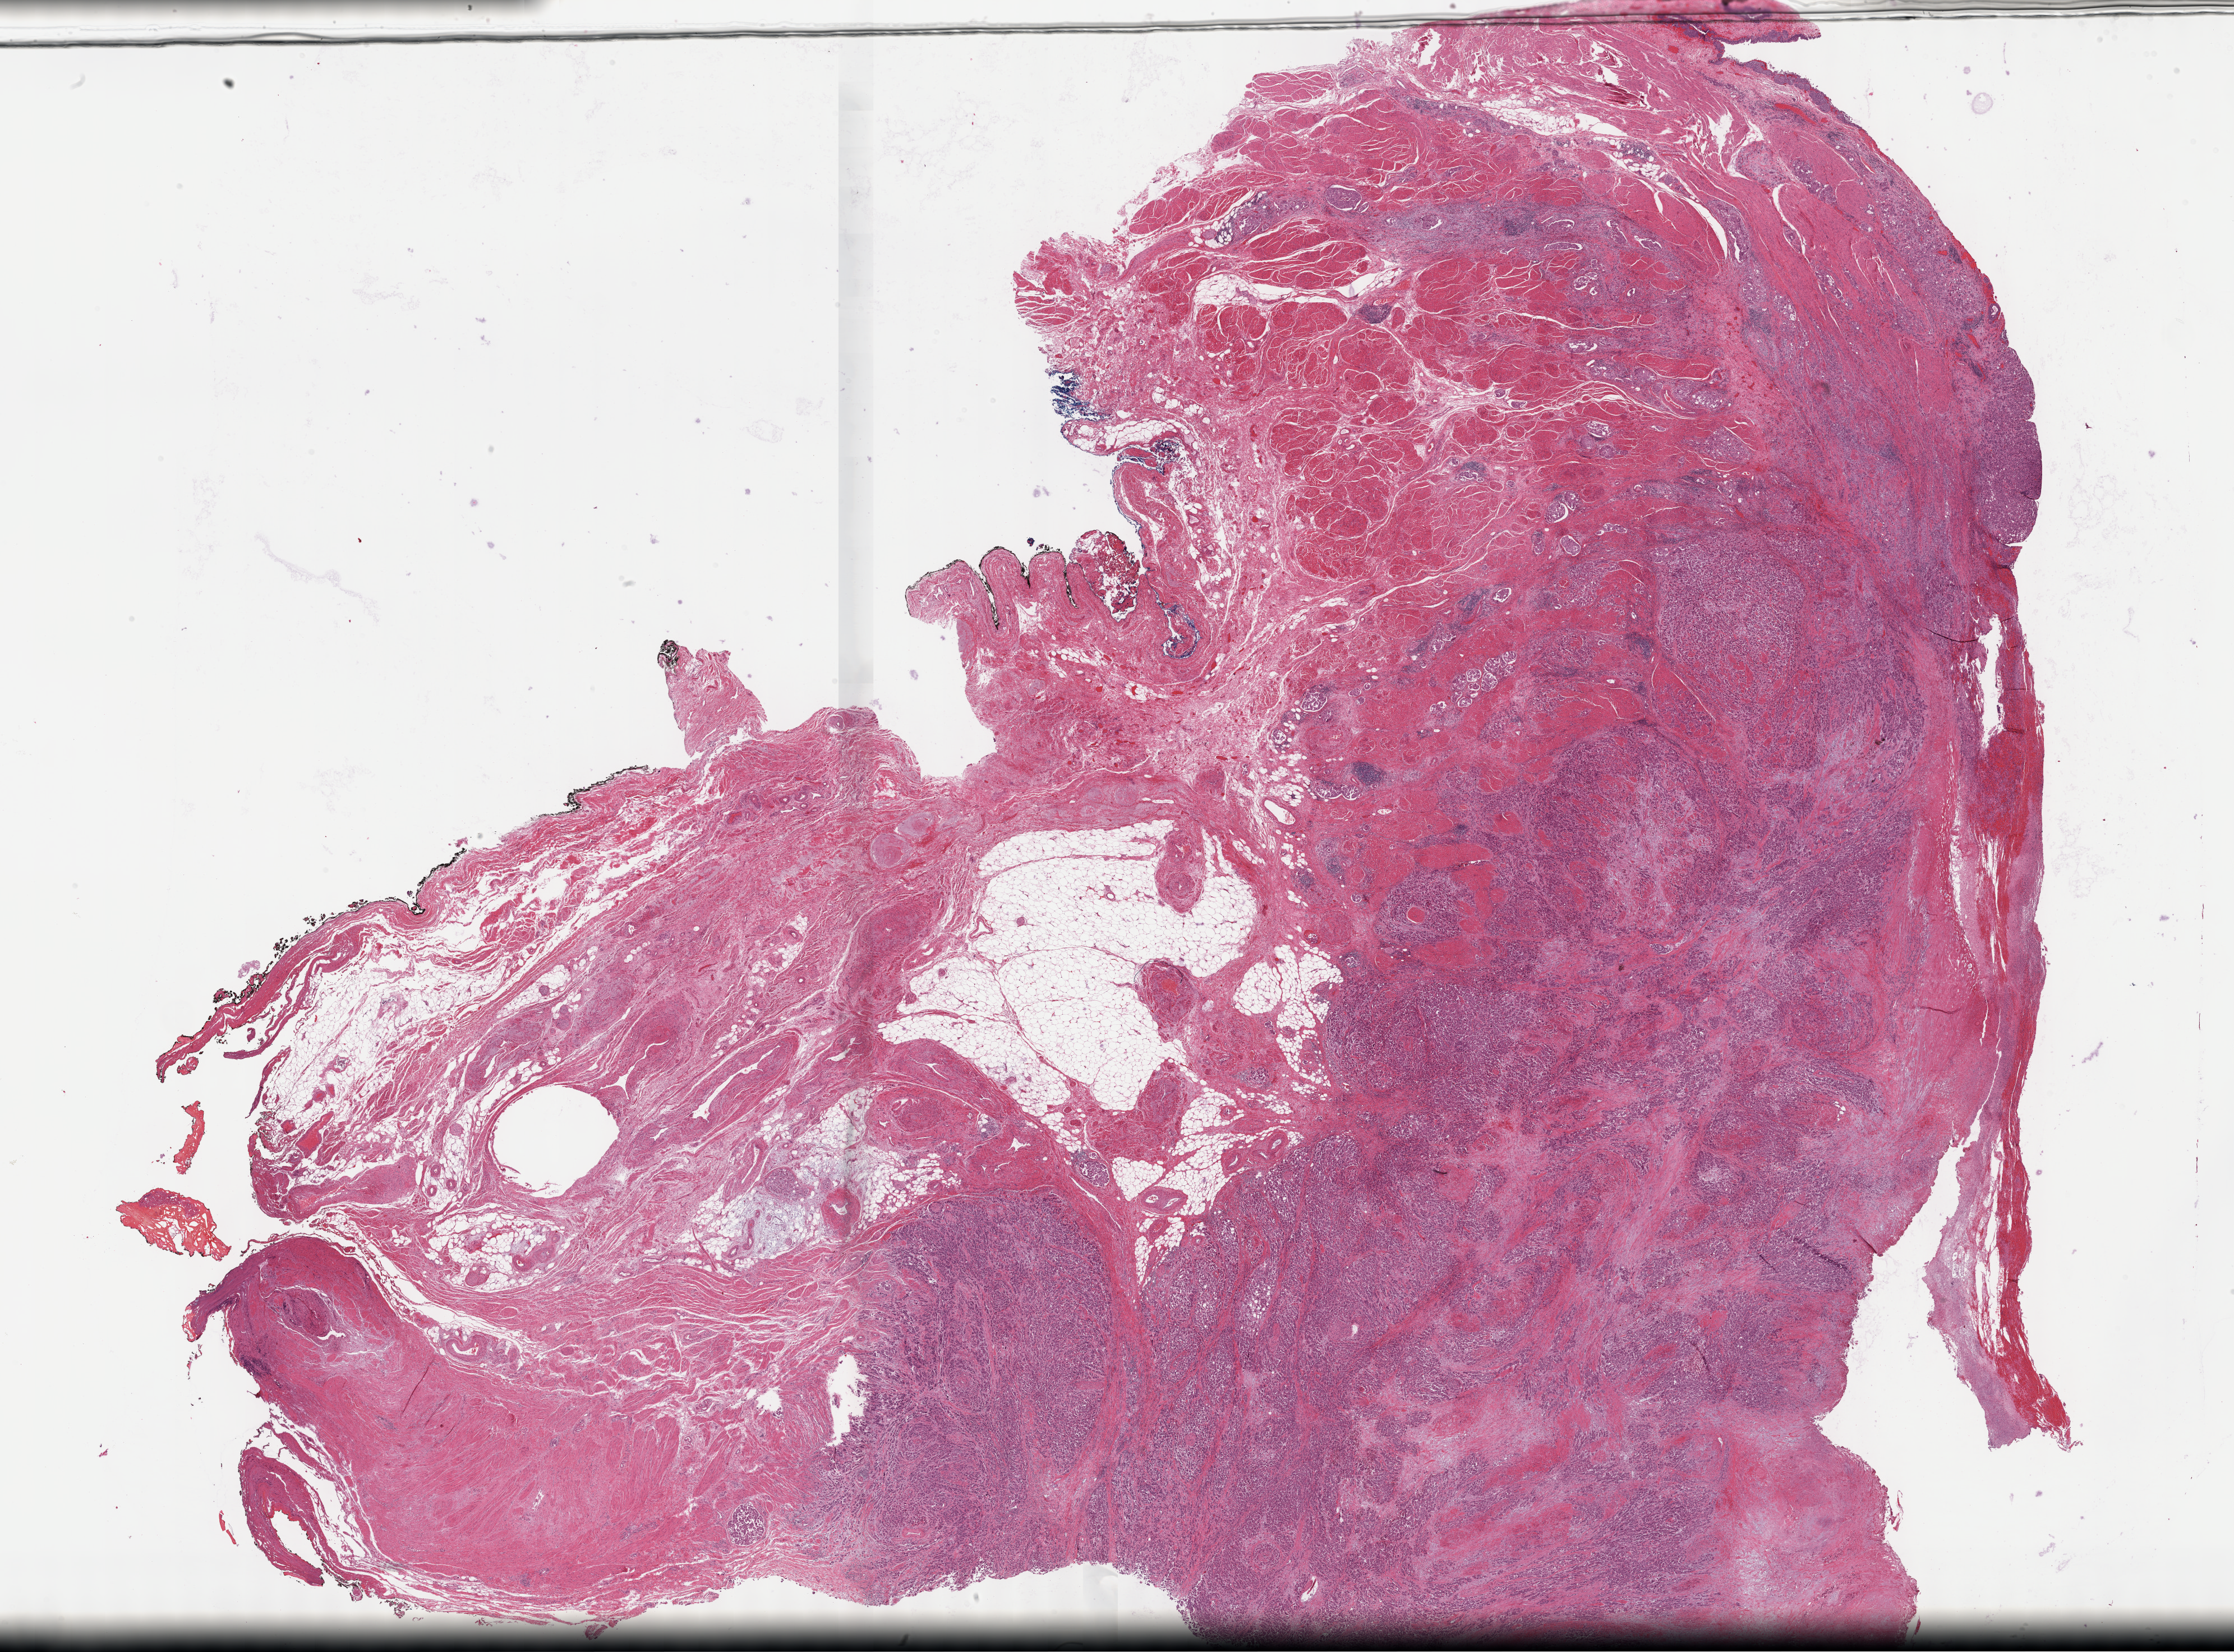
Whole-slide histology image, Hematoxylin and eosin (H&E) stained, low-resolution overview of the scanned area, about 32.2 x 23.8 mm (acquisition: 40x scan), FFPE section, sample: primary tumour, bladder. Patient: female, age at initial diagnosis 80 years. Histologic grade: high grade.
* AJCC pathologic stage: IV (7th edition)
* histologic diagnosis: Transitional cell carcinoma (lateral wall of bladder)
* lymph nodes positive (case pathology): 11 of 11 examined